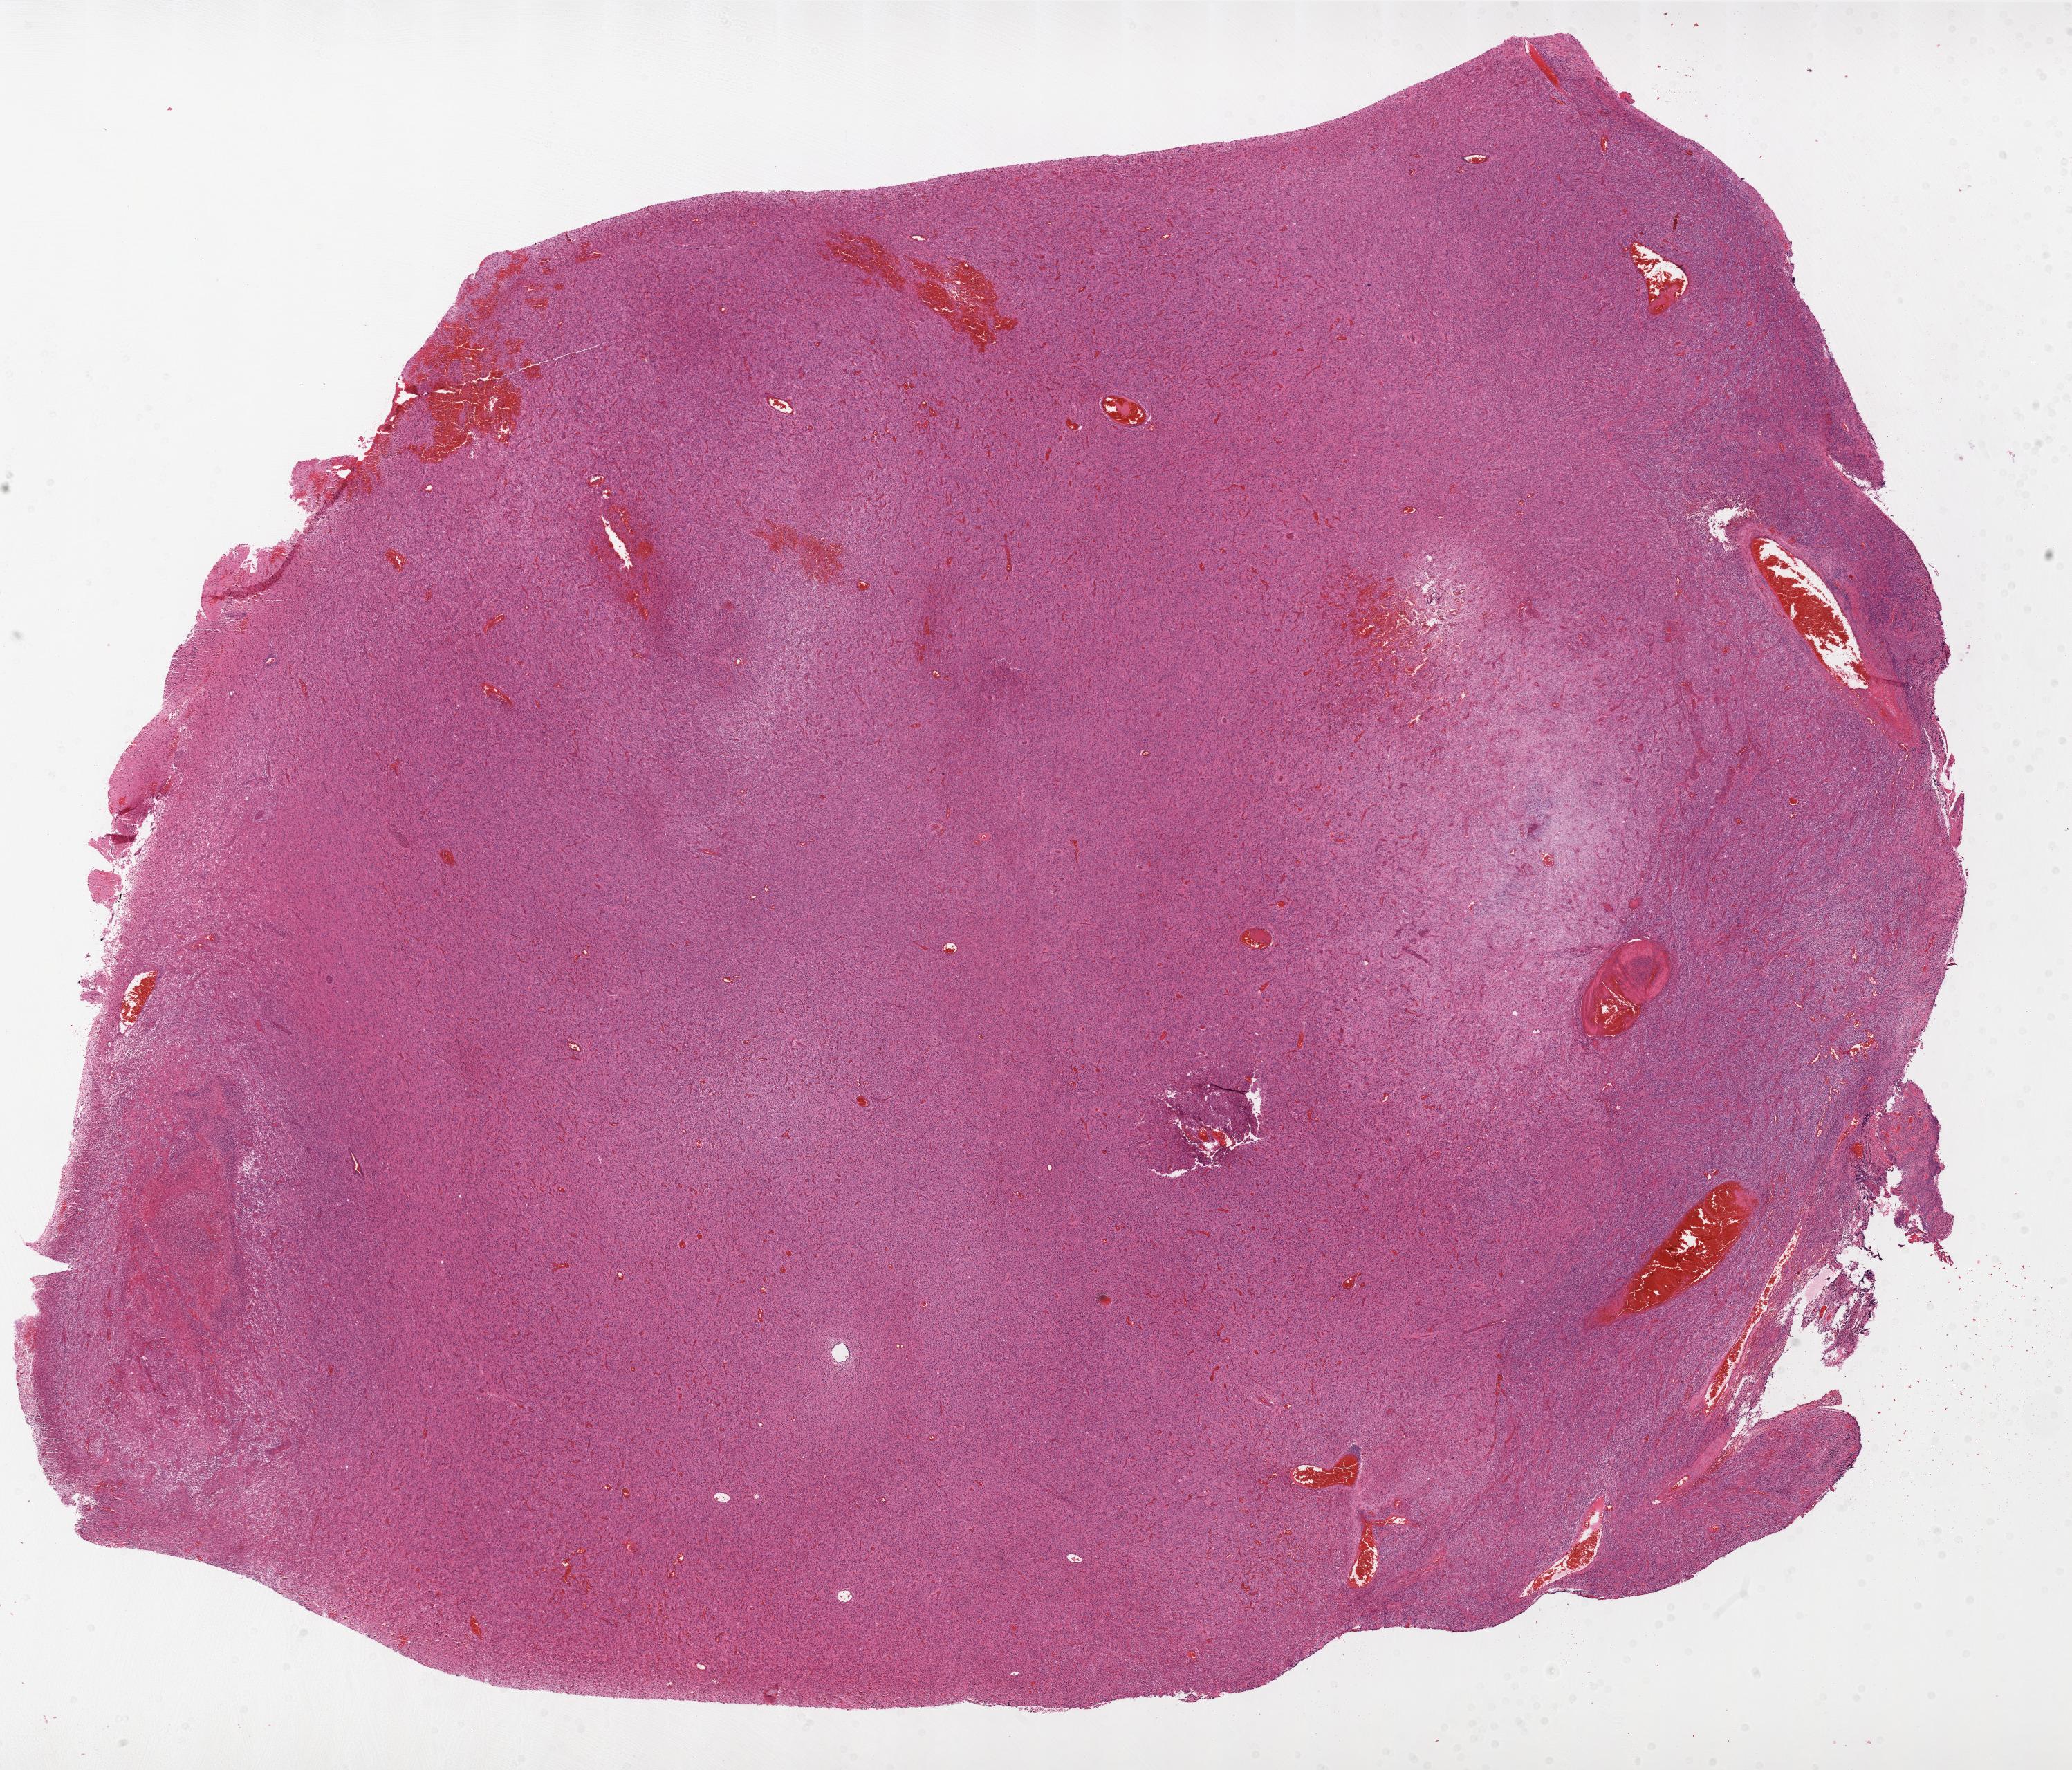
Digitized H&E-stained tissue section (whole slide), shown as a low-resolution overview of the whole scanned area (about 24.0 x 20.5 mm, from a 20x scan), formalin-fixed paraffin-embedded (FFPE) diagnostic section, sample: primary tumour, brain. Female, age 52 years at initial diagnosis.
- pathologic diagnosis: Glioblastoma